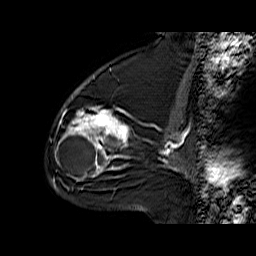
Breast MRI (dynamic contrast-enhanced), one sagittal slice. Position 38 of 60 along the scan axis. Dynamic contrast-enhanced series, time point 2 of 6 at this slice position (early post-contrast). 1.5 T. TE 6.3 ms, TR 32.9 ms. 256 × 256 image matrix. Female patient. Case-level facts recorded for this patient, not image findings: setting: breast cancer imaged before/during neoadjuvant chemotherapy; receptor status: triple-negative.
Outlined on this slice (semi-automatic segmentation, software-assisted and operator-edited):
- analysis volume of interest (the breast-tissue region the enhancement analysis was run in; not a lesion): bounding box [x1, y1, x2, y2] px = [56, 76, 132, 170]
- tumour enhancement mask (voxels above the 100 % enhancement threshold inside the analysis volume of interest): [59, 107, 129, 170]